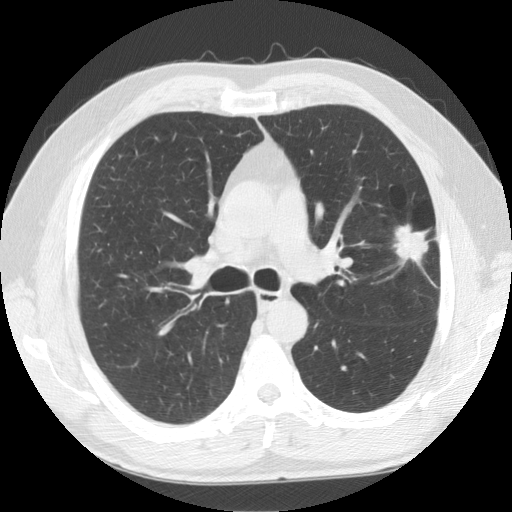
Chest CT (low-dose screening protocol), one axial image, baseline screening round, lung window (W 1500 / L -600 HU), standard (soft-tissue) reconstruction kernel (STANDARD), 512 × 512 image matrix, field of view 360 × 360 mm. Male, age 59 years at enrolment. Former smoker at enrolment.
Expert reader's lesion annotation, box from (x=375, y=204) to (x=456, y=283) px. Screening reader's record for this exam (one nodule recorded; not confirmed to be the boxed lesion): non-calcified nodule or mass ≥4 mm, left upper lobe, 23 × 23 mm, spiculated (stellate) margins, soft tissue attenuation. Official screen result: positive, change unspecified: nodule(s) >= 4 mm or enlarging nodule(s), mass(es), or other non-specific abnormalities suspicious for lung cancer.